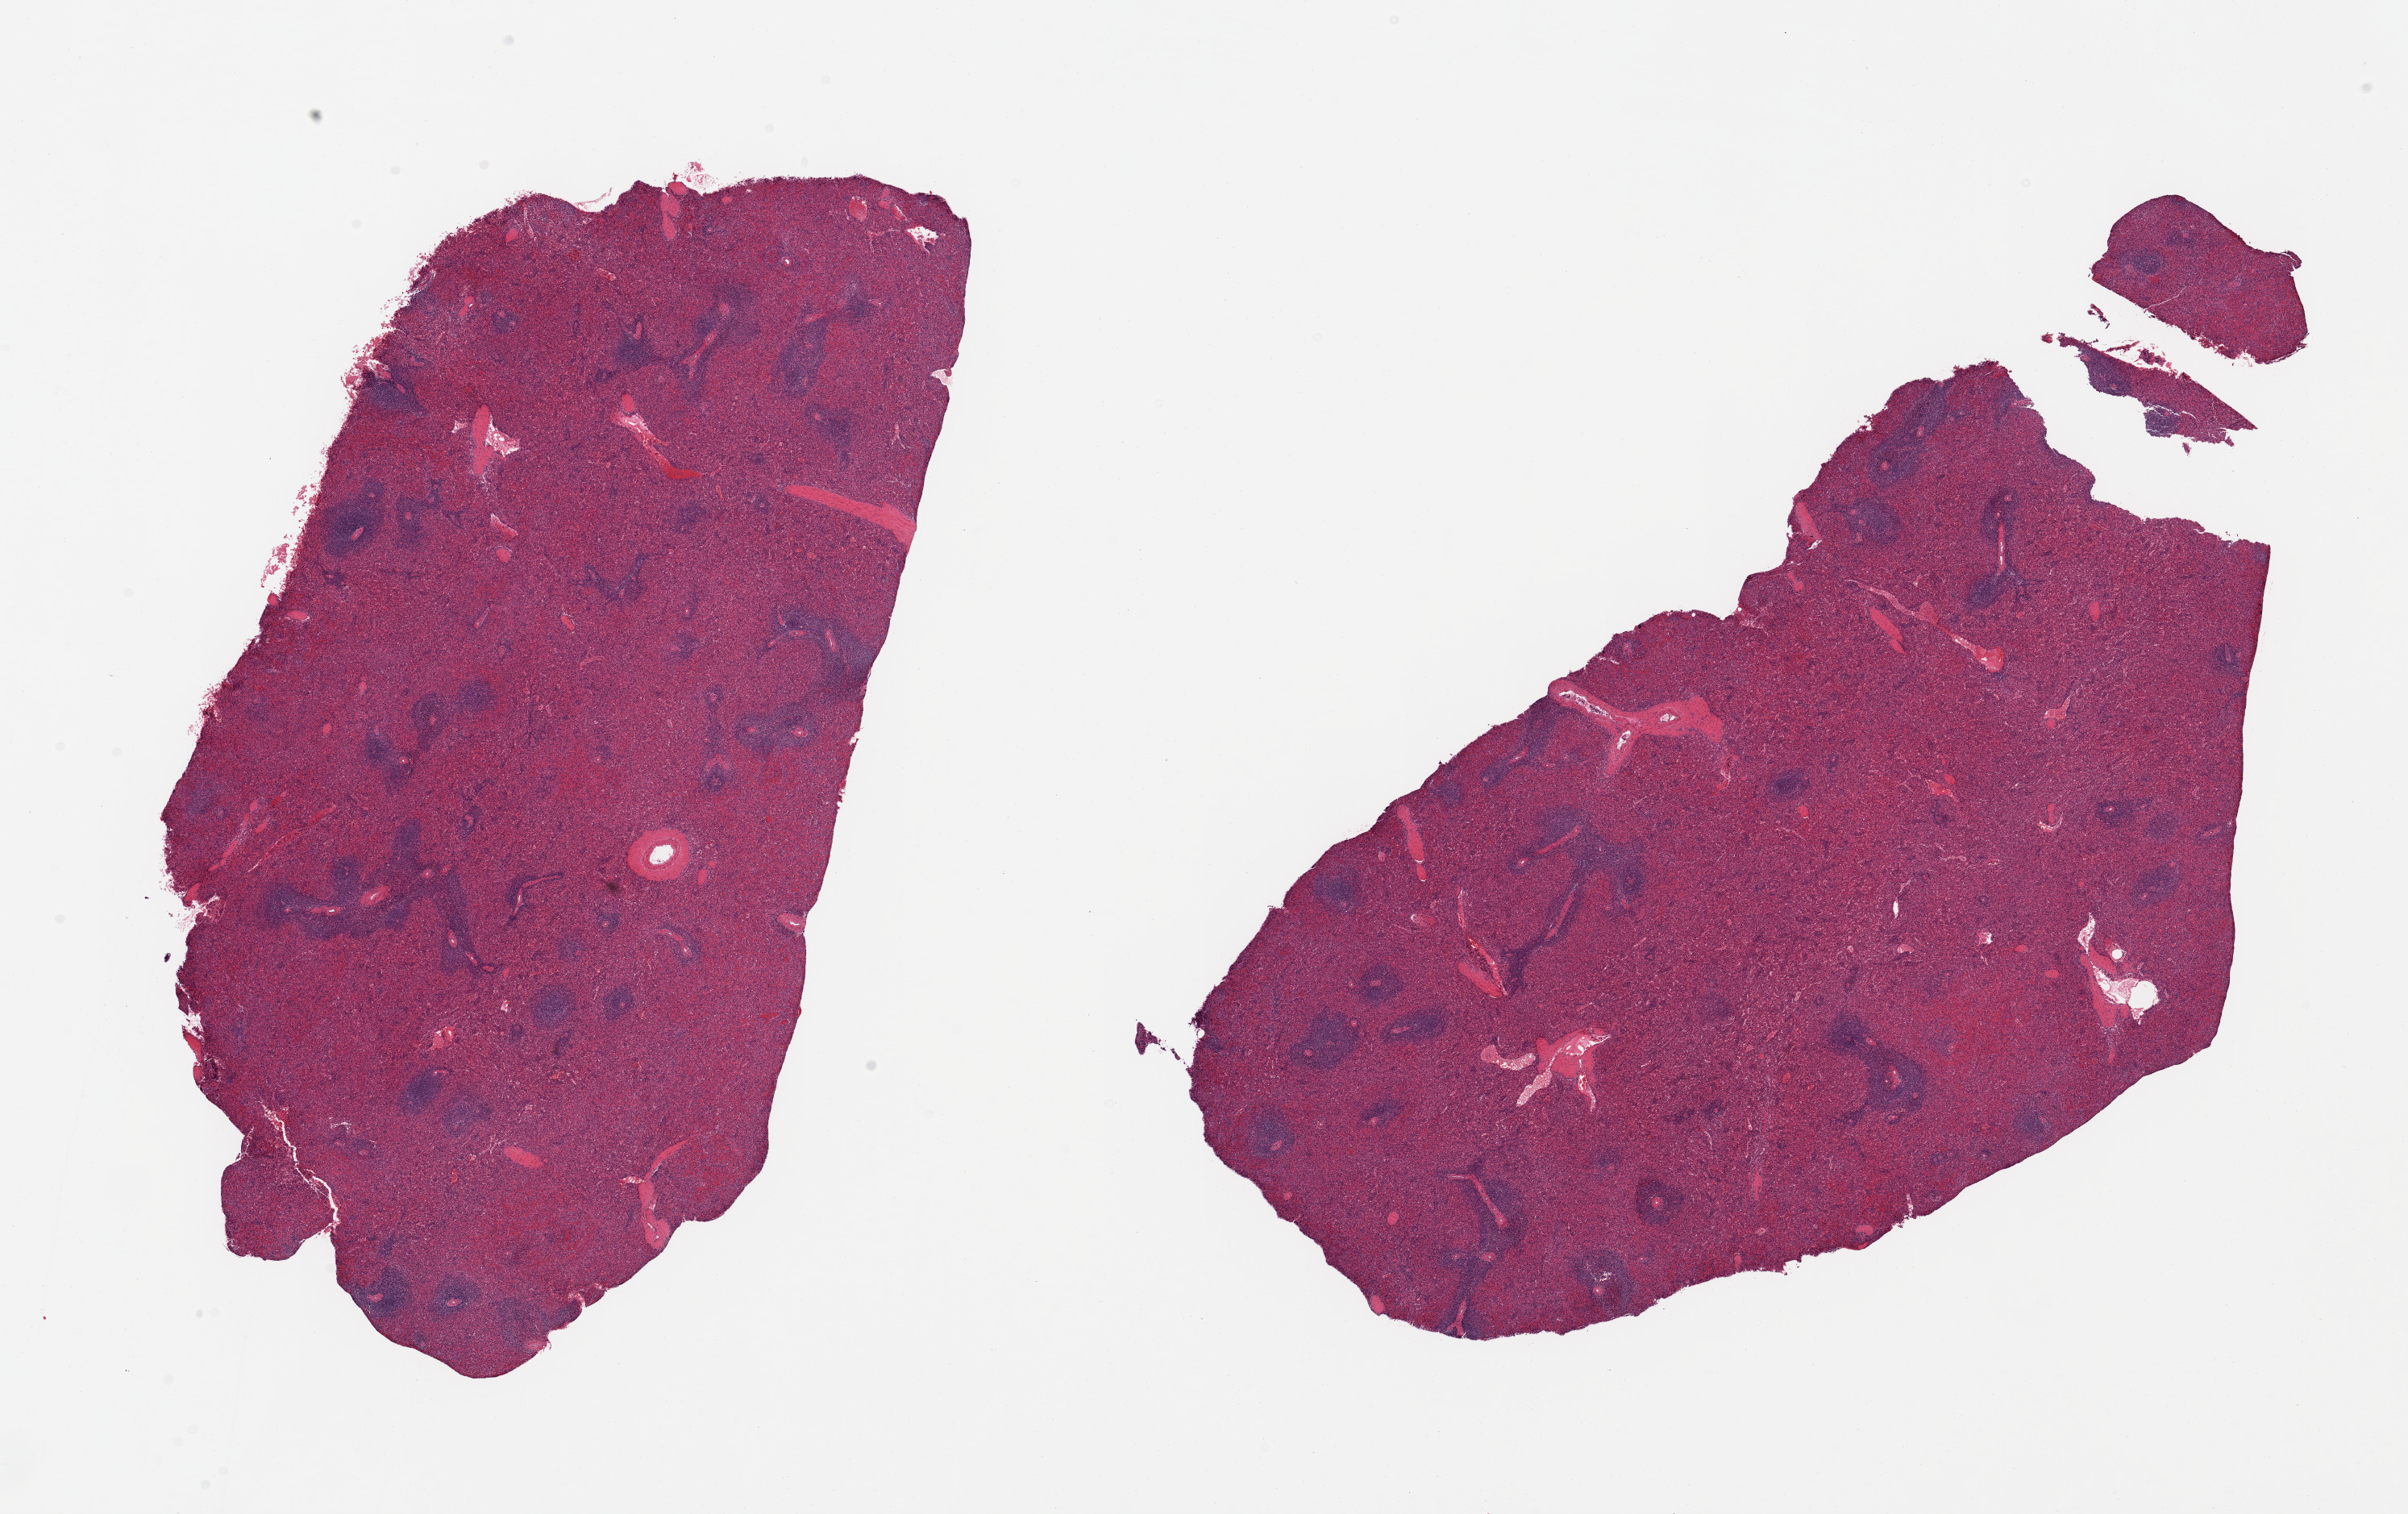
Digitized H&E-stained section — shown as a low-resolution overview of the whole scanned area (about 23.6 x 14.9 mm). PAXgene-fixed, paraffin-embedded tissue. Section of spleen (target tissue). Donor tissue sample. Male donor.
Pathologist's review note for this sample: 2 pieces, no abnormalities.